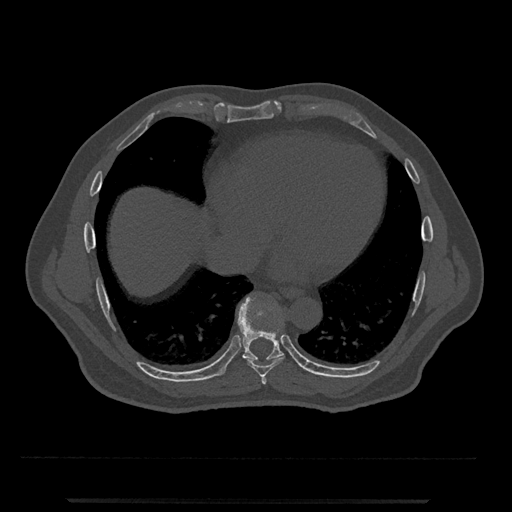
CT including the spine, one axial slice; position 601 of 797 along the scan axis; reconstruction kernel Br40s/3; 120 kVp; bone window (W 1800 / L 400 HU); 0.5 mm slice thickness; 512 × 512 image matrix, field of view 419 × 419 mm. Male patient, age 63 years. From the clinical record (not read from this slice): primary cancer: prostate.
Structures marked on this image (semi-automatically segmented with operator editing):
- T7 vertebra: box from (x=261, y=376) to (x=267, y=385) px
- T8 vertebra: (x=248, y=355)–(x=284, y=377)
- T9 vertebra: (x=221, y=296)–(x=284, y=375)